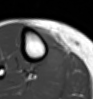
MRI of an extremity soft-tissue mass, one axial slice; position 24 of 54 along the scan axis; MR volume resampled by the dataset authors to the PET/CT grid (not the native acquisition matrix); 3.27 mm slice thickness; 93 × 99 image matrix, field of view 91 × 97 mm. Female patient. Case-level facts recorded for this patient, not image findings: histological type: undifferentiated – high grade; grade: high; site of the primary tumour: right thigh.
Outlined on this slice (expert contour drawn on MRI and transferred to this co-registered scan by the dataset authors):
- gross tumour volume (mass): bounding box [x1, y1, x2, y2] px = [32, 25, 64, 71]